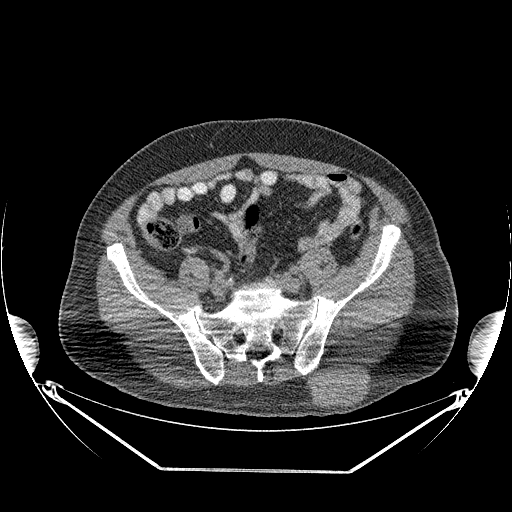
CT of an extremity soft-tissue mass (from a PET/CT study), one axial slice; position 87 of 267 along the scan axis; reconstruction kernel STANDARD; soft-tissue window (W 400 / L 40 HU); 3.75 mm slice thickness; 512 × 512 image matrix, field of view 500 × 500 mm. Male patient. Case-level facts recorded for this patient, not image findings: histological type: pleiomorphic leiomyosarcoma; grade: high; site of the primary tumour: left buttock.
Outlined on this slice (expert contour drawn on MRI and transferred to this co-registered scan by the dataset authors):
- gross tumour volume including surrounding oedema: bounding box (x1, y1, x2, y2) in pixels: (310, 368, 368, 407)
- gross tumour volume (mass): (310, 368, 368, 407)